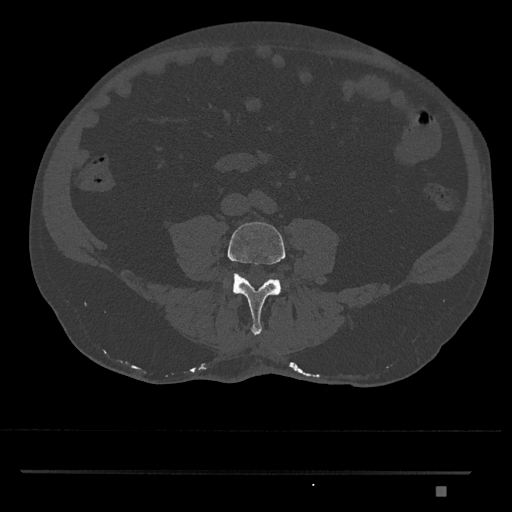
CT including the spine, one axial slice; position 608 of 1134 along the scan axis; reconstruction kernel Br40s/3; 120 kVp; bone window (W 1800 / L 400 HU); 0.5 mm slice thickness; 512 × 512 image matrix, field of view 429 × 429 mm. Patient: male, 65 years. Case-level facts recorded for this patient, not image findings: primary cancer: prostate.
Structures marked on this image (semi-automatically segmented with operator editing):
- L4 vertebra: bounding box (x1, y1, x2, y2) in pixels: (224, 222, 286, 335)